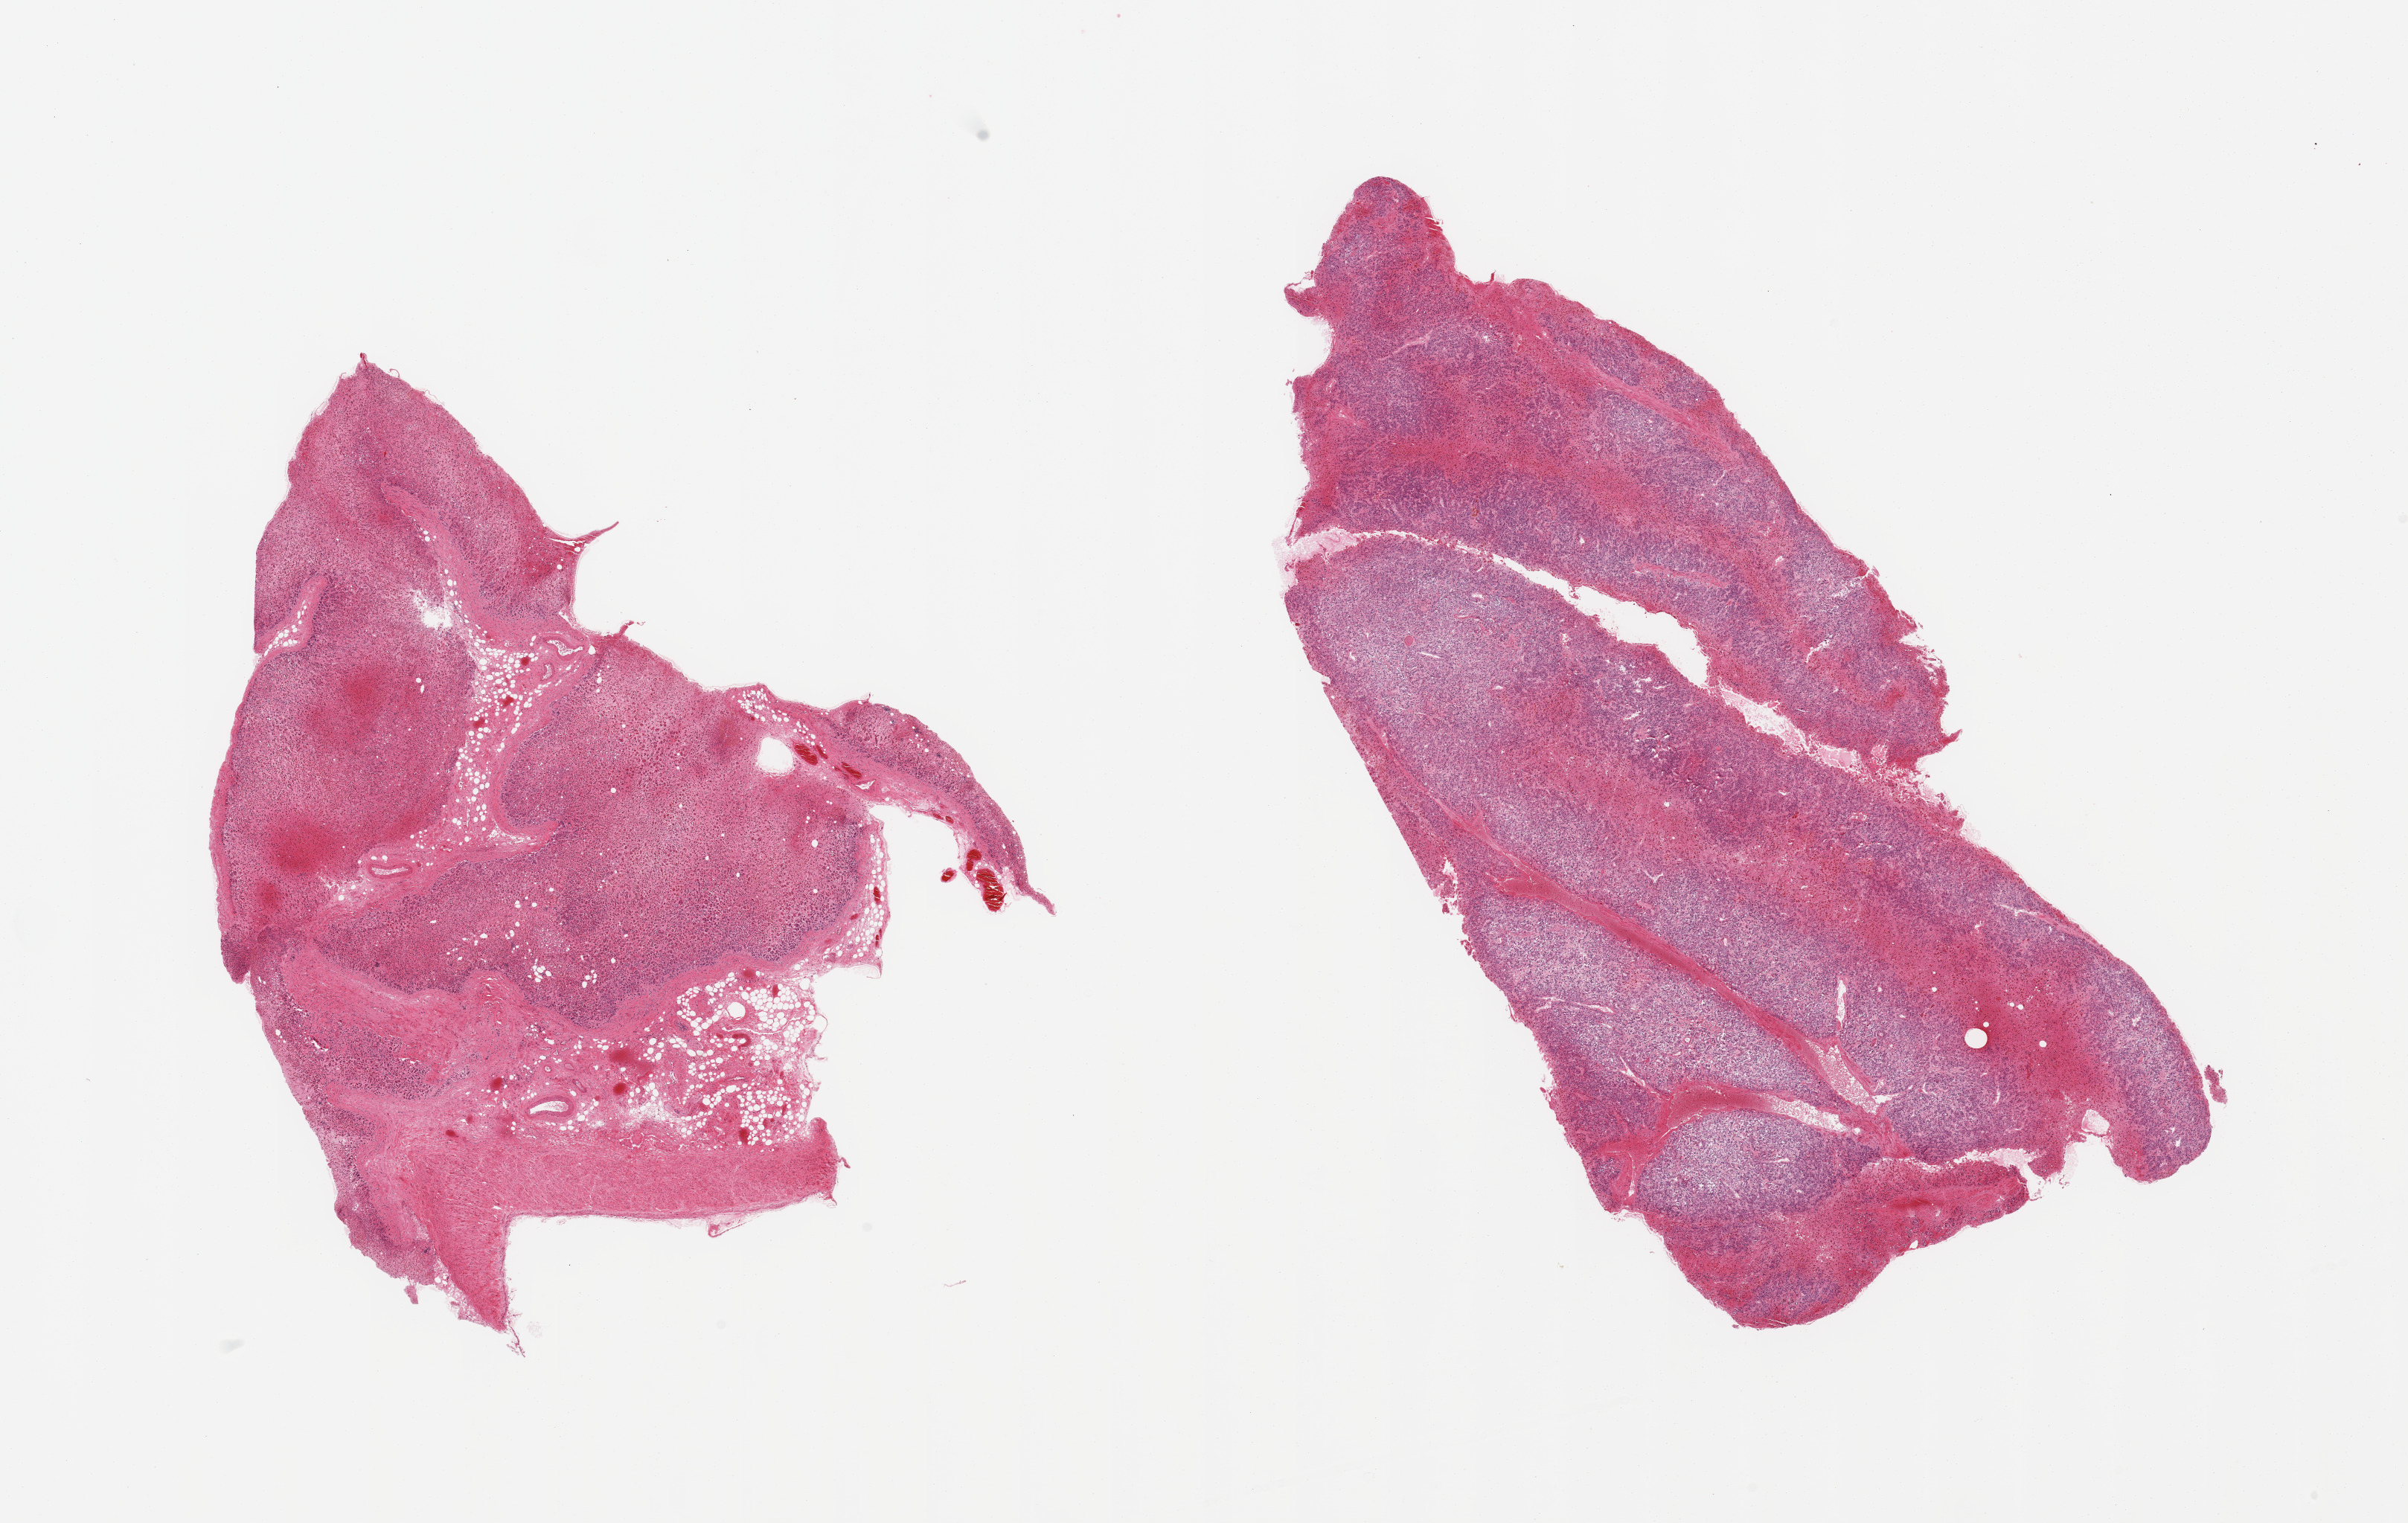
Whole-slide image, haematoxylin and eosin stain, brightfield — shown as a low-resolution overview of the whole scanned area (about 25.6 x 16.2 mm, acquisition: 20x scan); PAXgene-fixed, paraffin-embedded tissue; sampled site (target tissue): adrenal gland; donor tissue sample. Male donor.
* pathologist's review note for this sample: 2 pieces; moderately autolyzed with hemorrhage, 1 piece is cortex, 2nd is largely medulla and suggestive of medullary hyperplasia